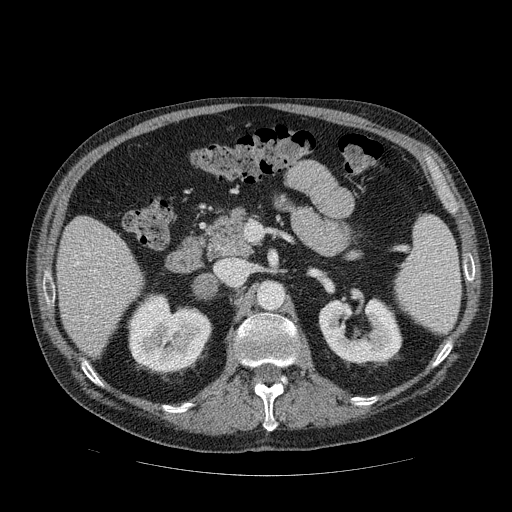
Contrast-enhanced abdominal CT, one axial slice; slice 45 of 111 in the series (ordered by position); 120 kVp; intravenous contrast given; soft-tissue window (W 400 / L 40 HU); 2.5 mm slice thickness; 512 × 512 image matrix. Male patient, age 56 years. Case-level facts recorded for this patient, not image findings: diagnosis: adrenocortical carcinoma; tumour side: right adrenal; tumour size at pathology: 9 cm; Ki-67 index: 48 %; stage (as recorded): 4.
Annotated regions visible in this slice (semi-automatically segmented with operator editing):
- mass: bounding box [x1, y1, x2, y2] px = [193, 274, 216, 297]